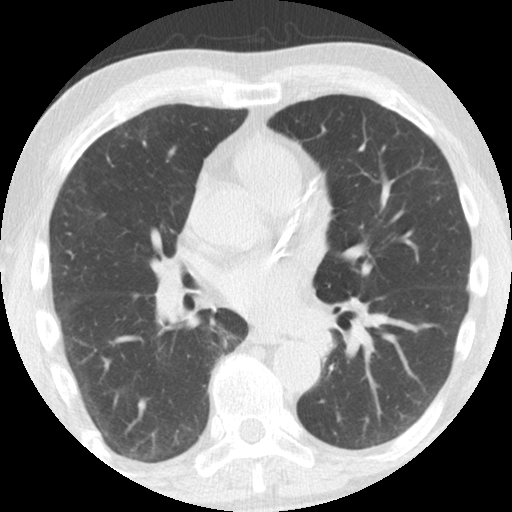
Axial slice from a low-dose chest CT screening exam; third screening round (two years after baseline); lung window (W 1500 / L -600 HU); 2.5 mm slice thickness. Male, age 61 years at enrolment. Former smoker at enrolment.
Expert-annotated lung lesion, box from (x=296, y=317) to (x=345, y=363) px. No non-calcified nodule or mass ≥4 mm was recorded by the screening reader at this exam. Later outcome: lung cancer diagnosed 363 days after this screen — squamous cell carcinoma, NOS, left upper lobe, left lower lobe, well differentiated (G1), stage IIB (AJCC 6th edition), 100 mm at pathology.